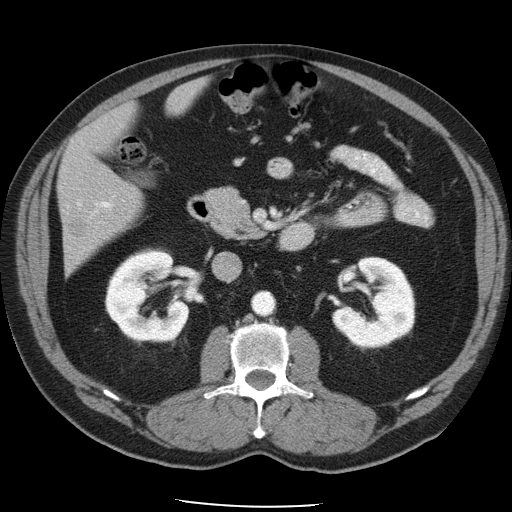
Contrast-enhanced abdominal CT, one axial slice; slice 21 of 49 in the series (ordered by position); reconstruction kernel STANDARD; 120 kVp; intravenous contrast given; soft-tissue window (W 400 / L 40 HU); 5 mm slice thickness; 512 × 512 image matrix, field of view 395 × 395 mm. Male patient, age 68 years. From the clinical record (not read from this slice): diagnosis: colorectal cancer liver metastases, imaged before liver resection; multiple liver metastases: yes; largest metastasis: 1.7 cm; disease in both lobes: no.
Annotated regions visible in this slice (manually delineated by an expert):
- hepatic veins: box from (x=78, y=201) to (x=82, y=206) px
- liver: (x=59, y=82)–(x=202, y=271)
- planned liver remnant (the part of the liver to remain after resection): (x=62, y=82)–(x=201, y=227)
- portal vein (with intrahepatic branches): (x=67, y=202)–(x=112, y=214)
- liver metastasis: (x=69, y=219)–(x=88, y=237)